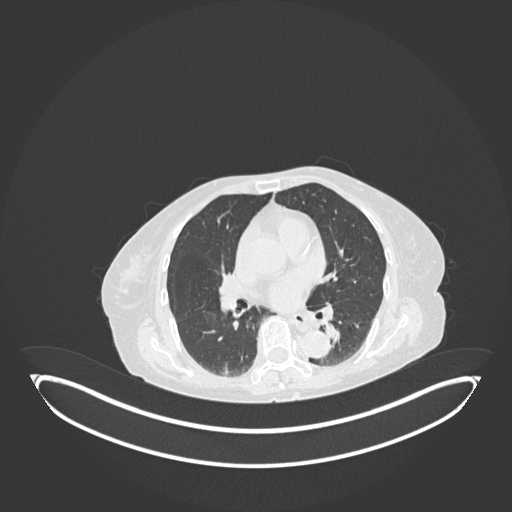
Chest CT, one axial slice. Slice 64 of 189 in the series (ordered by position). Reconstruction kernel B30f. 120 kVp. Lung window (W 1500 / L -600 HU). 1 mm slice thickness. 512 × 512 image matrix. Female patient, age 82 years. Case-level facts recorded for this patient, not image findings: clinical TNM (as recorded): T1b N0 M1.
Annotated regions visible in this slice (bounding box drawn by a radiologist):
- lung tumour (recorded histology: adenocarcinoma): box from (x=319, y=315) to (x=345, y=349) px